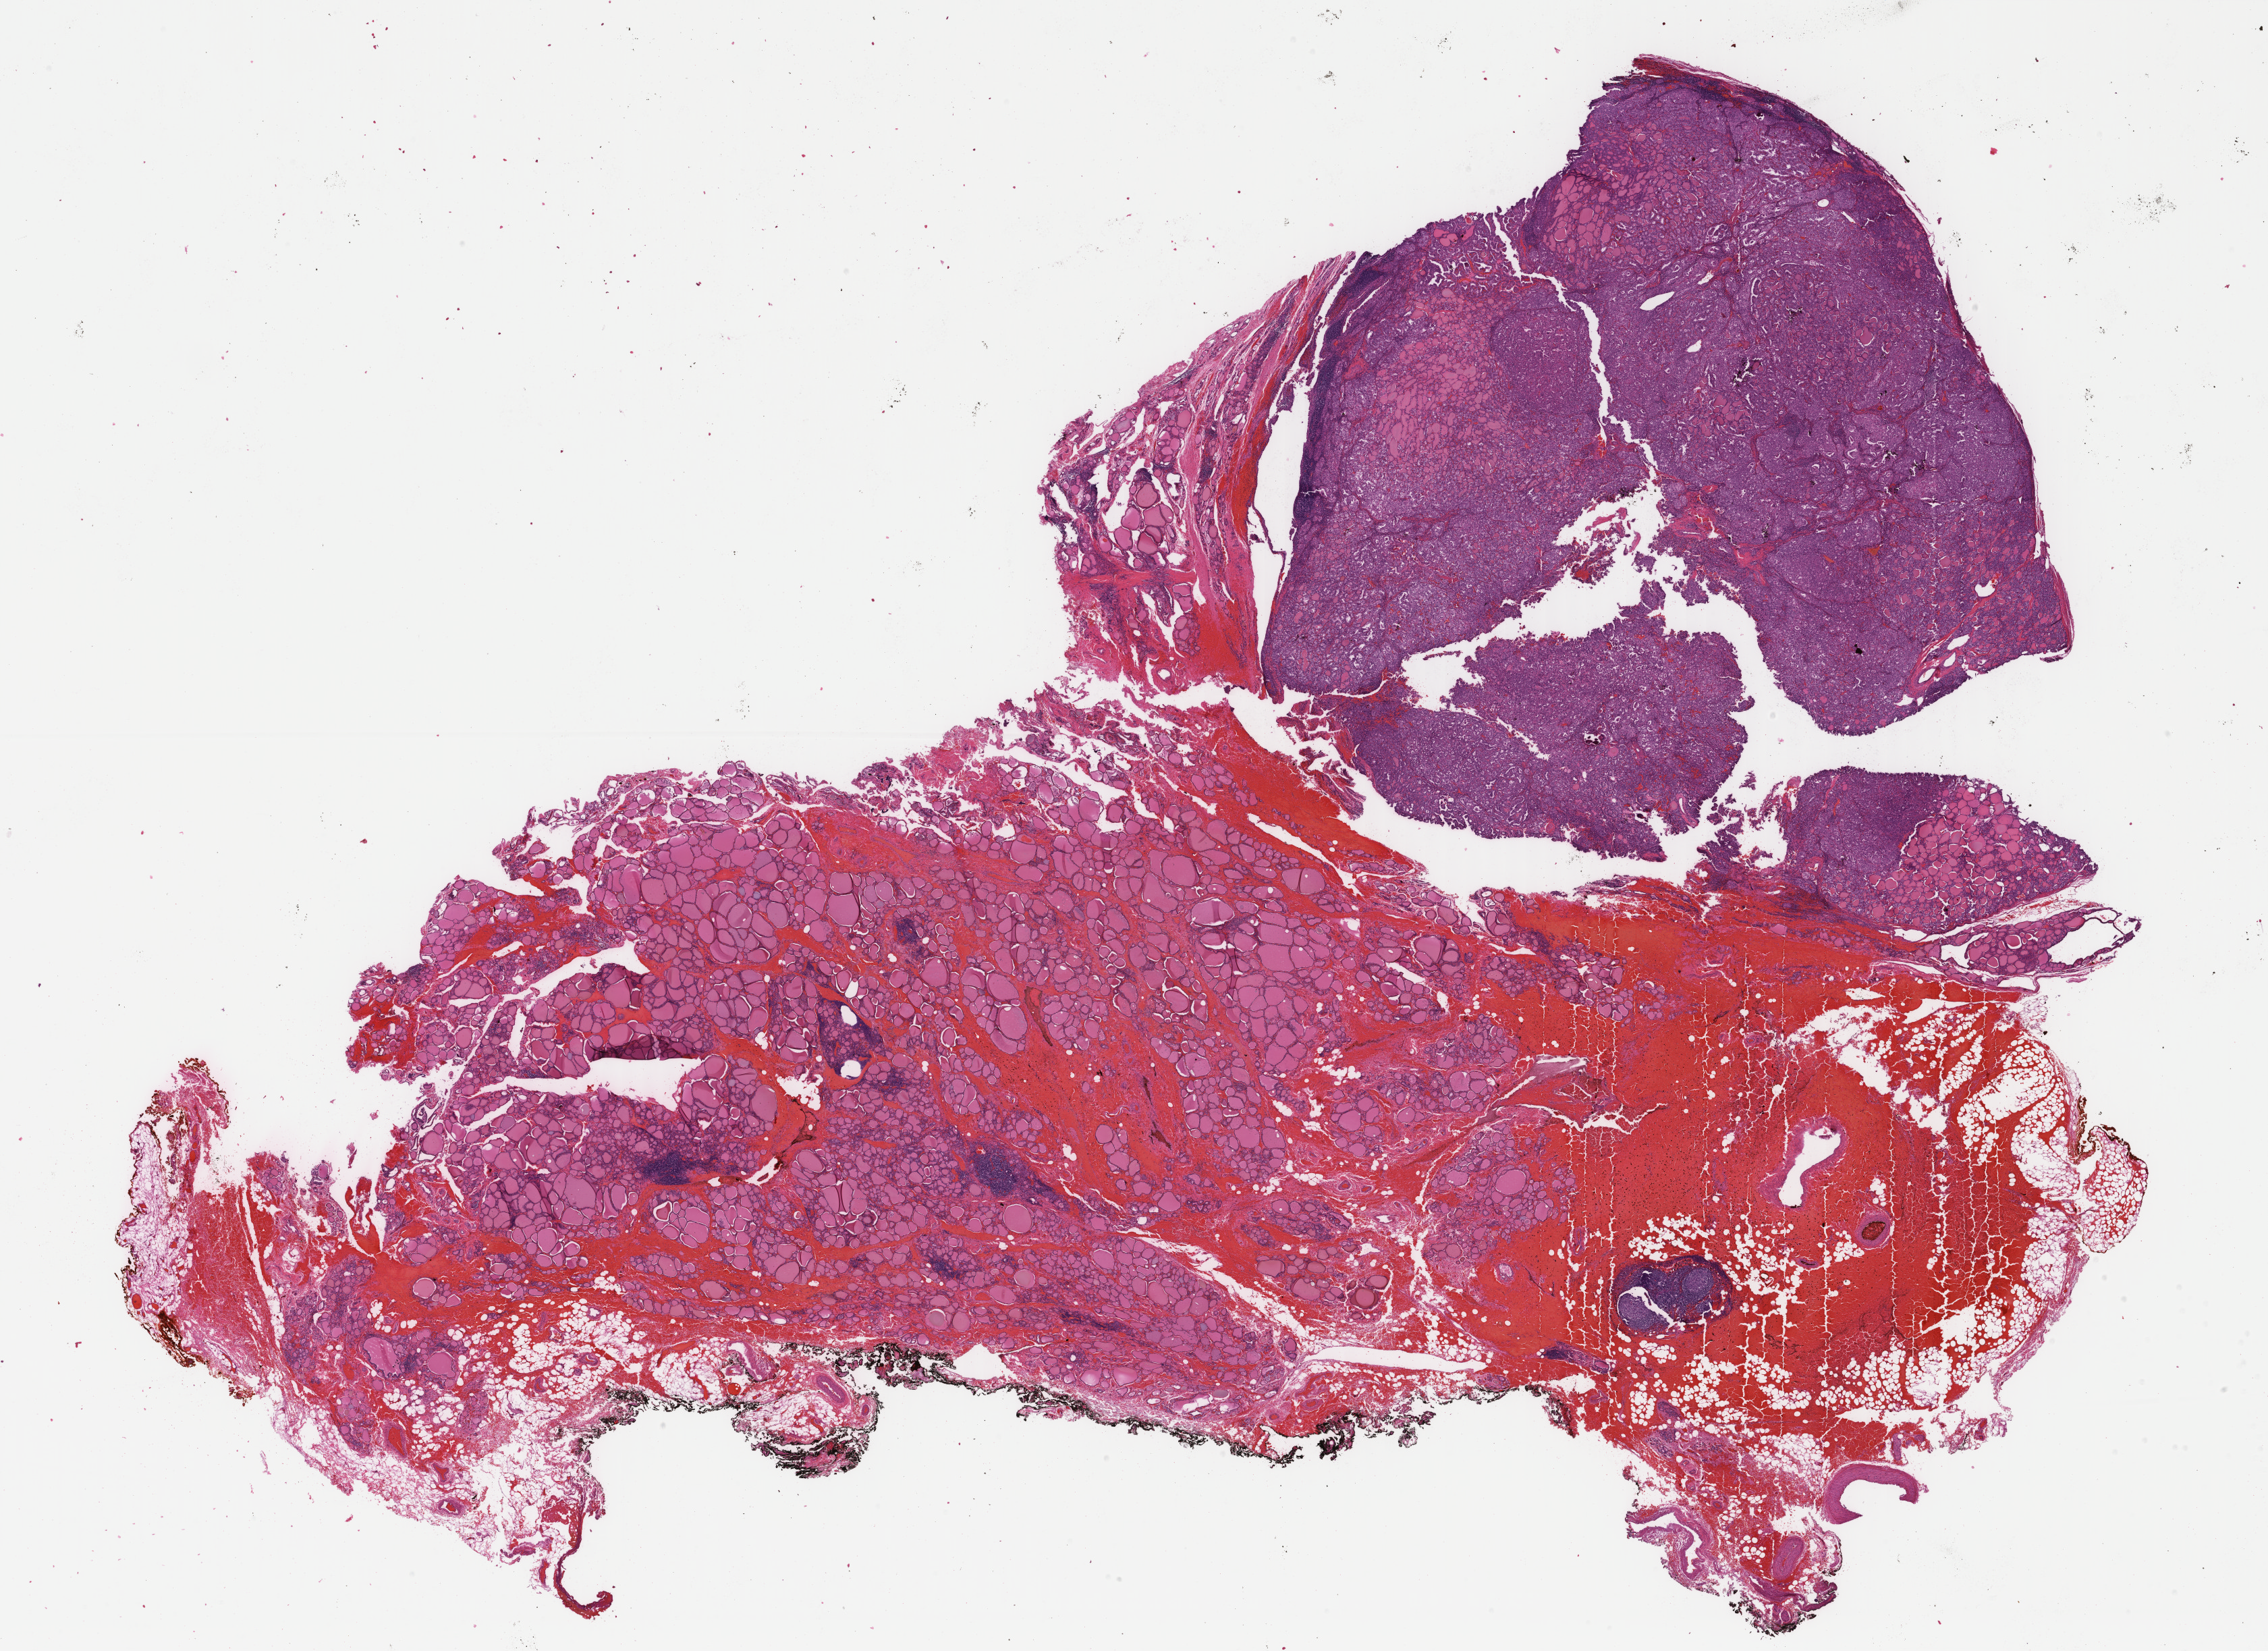
Digitized H&E tissue section (whole slide) — a low-resolution overview of the entire scanned area, about 26.7 x 19.4 mm (slide scanned at 40x), formalin-fixed paraffin-embedded (FFPE) diagnostic section, thyroid, primary tumour sample. Patient: male, age at initial diagnosis 62 years.
• pathologic diagnosis: Papillary adenocarcinoma, NOS (thyroid gland)
• AJCC pathologic stage: II (7th edition)
• lymph nodes positive (case pathology): 0 of 12 examined